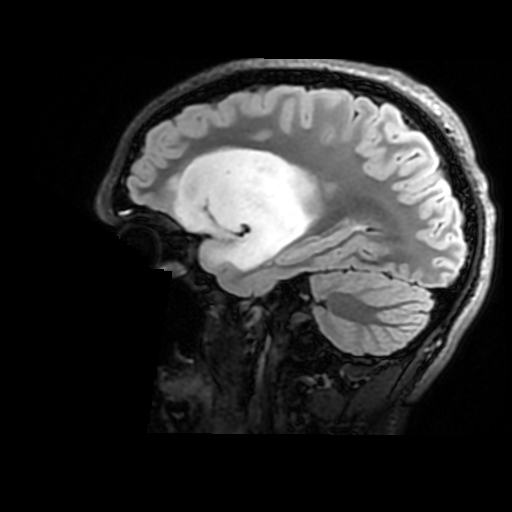
Brain MRI from a brain-tumour surgery series, one sagittal slice; slice 117 of 176 in the series (ordered by position); T2 FLAIR; 1 mm slice thickness; 512 × 512 image matrix. From the clinical record (not read from this slice): histopathology: Astrocytoma; WHO grade: 2; IDH mutation: yes; tumour location: Right Insular.
Outlined on this slice (outlined manually by an expert reader):
- tumour: bounding box (x1, y1, x2, y2) in pixels: (176, 147, 318, 273)